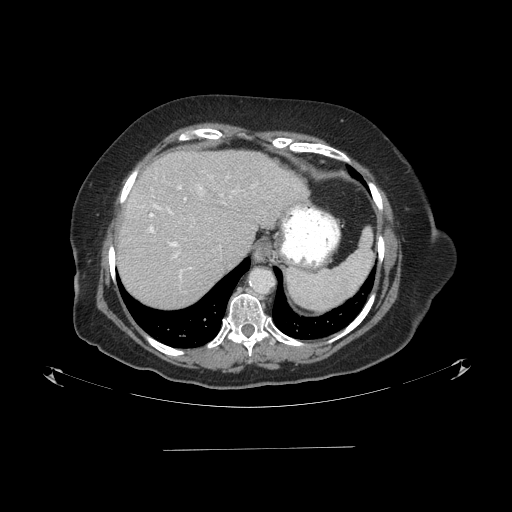
Contrast-enhanced abdominal CT (liver protocol), one axial slice; slice 70 of 103 in the series (ordered by position); one of 2 acquisitions stored at this slice position; soft-tissue window (W 400 / L 40 HU); 512 × 512 image matrix, field of view 500 × 500 mm. From the clinical record (not read from this slice): diagnosis: hepatocellular carcinoma (patient treated with transarterial chemoembolisation; whether this scan precedes or follows treatment is not stated here); TNM stage (as recorded): Stage-IIIA; Child-Pugh class: A; tumour differentiation: poorly differentiated; tumour size: 5.2 cm.
Outlined on this slice (semi-automatically segmented with operator editing):
- liver parenchyma outside the tumour (the mass and vessels are separate outlines, so this box may not span the whole liver): bounding box [x1, y1, x2, y2] px = [116, 150, 308, 306]
- liver vessels: [148, 185, 235, 279]